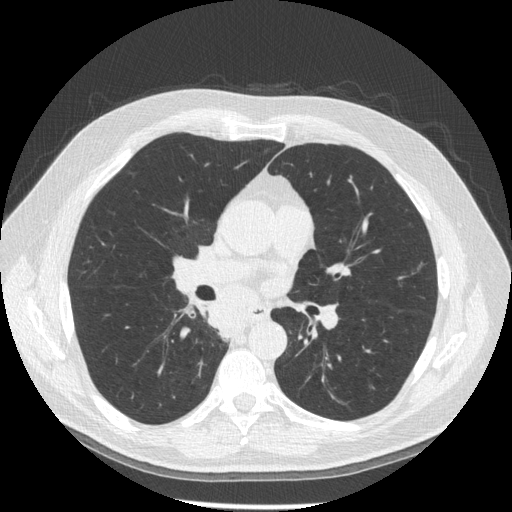
Low-dose screening chest CT, one axial slice. Slice 100 of 181 in the series (ordered by position). Reconstruction kernel STANDARD. 120 kVp. Lung window (W 1500 / L -600 HU). 512 × 512 image matrix.
Outlined on this slice (outlined manually by an expert reader):
- lesion 1 (tumor, lower lobe of right lung): box from (x=207, y=300) to (x=247, y=341) px